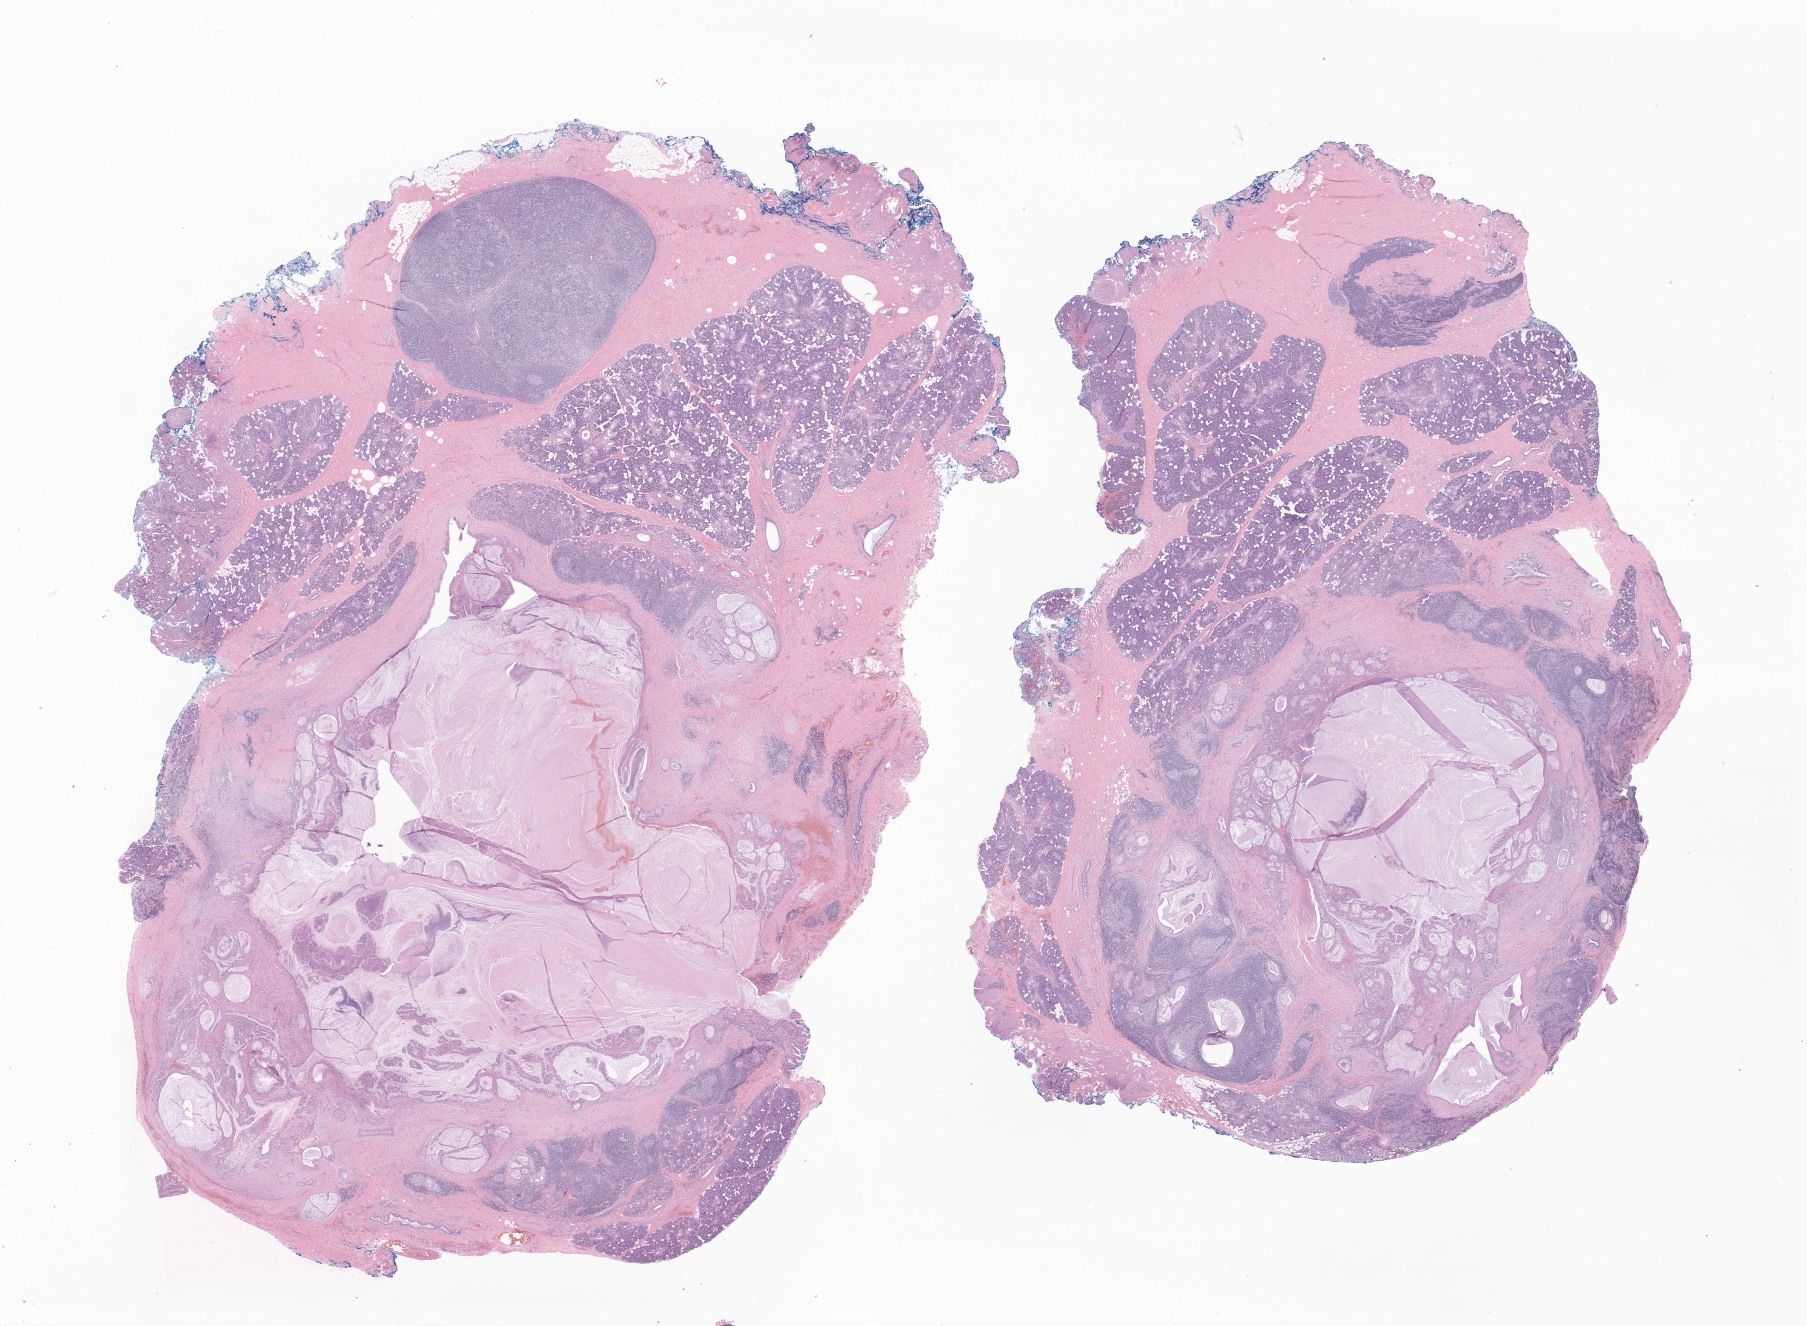
Digitized H&E-stained section of tumor tissue from the parotid gland — shown as a low-resolution overview of the whole scanned area (about 30.5 x 22.4 mm), formalin-fixed, paraffin-embedded (FFPE) tissue. Patient: female, age 156 months (13 years).
Diagnosis: Mucoepidermoid carcinoma.